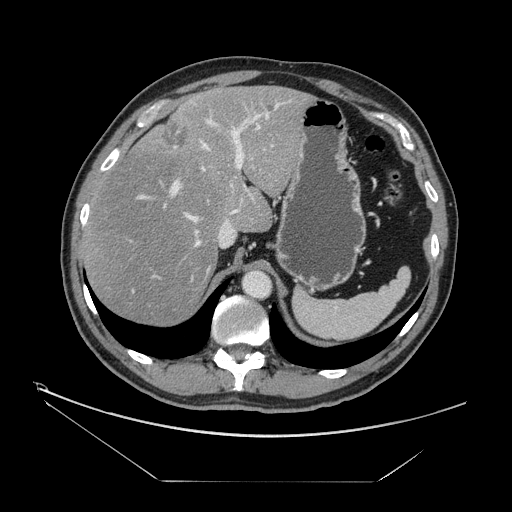
Contrast-enhanced abdominal CT, one axial slice; position 110 of 161 along the scan axis; reconstruction kernel STANDARD; 120 kVp; intravenous contrast given; soft-tissue window (W 400 / L 40 HU); 2.5 mm slice thickness; 512 × 512 image matrix, field of view 440 × 440 mm. Male patient, age 65 years. Case-level facts recorded for this patient, not image findings: diagnosis: colorectal cancer liver metastases, imaged before liver resection; multiple liver metastases: yes; largest metastasis: 4.2 cm; disease in both lobes: yes.
Structures marked on this image (expert manual segmentation):
- hepatic veins: bounding box [x1, y1, x2, y2] px = [187, 113, 268, 247]
- liver: [84, 87, 309, 326]
- planned liver remnant (the part of the liver to remain after resection): [84, 87, 309, 326]
- portal vein (with intrahepatic branches): [136, 100, 290, 213]
- liver metastasis: [161, 123, 190, 151]